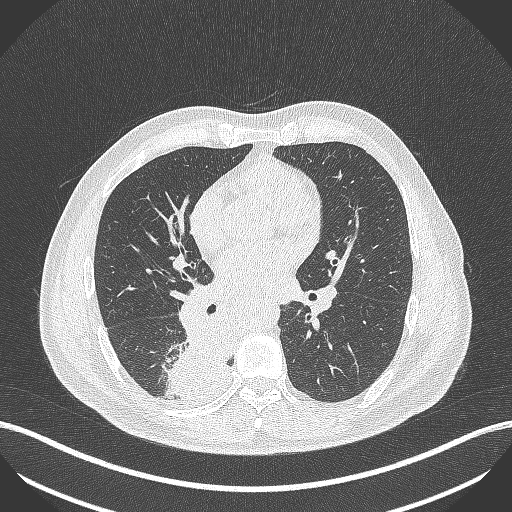
Chest CT, one axial slice; slice 234 of 451 in the series (ordered by position); reconstruction kernel B70f; lung window (W 1500 / L -600 HU); 512 × 512 image matrix. Patient: male, 61 years. From the clinical record (not read from this slice): clinical TNM (as recorded): T1 N0 M0; histopathological grade: G3.
Structures marked on this image (bounding box drawn by a radiologist):
- lung tumour (recorded histology: small cell carcinoma): bounding box [x1, y1, x2, y2] px = [164, 314, 231, 403]